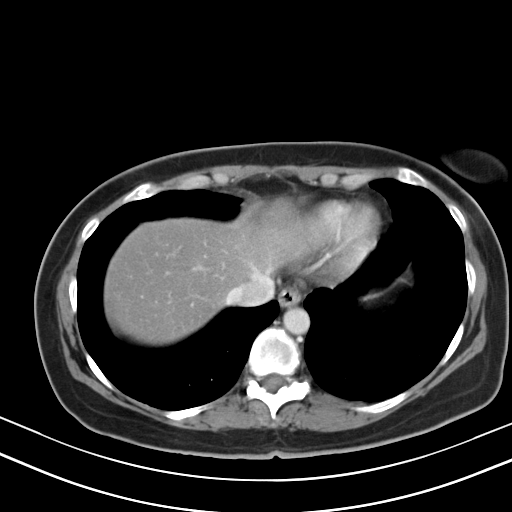
Contrast-enhanced abdominal CT, one axial slice; position 42 of 47 along the scan axis; reconstruction kernel B40s; soft-tissue window (W 400 / L 40 HU); 5 mm slice thickness; 512 × 512 image matrix, field of view 350 × 350 mm. Female patient. Case-level facts recorded for this patient, not image findings: diagnosis: colorectal cancer liver metastases, imaged before liver resection; multiple liver metastases: no; largest metastasis: 3.5 cm; disease in both lobes: no.
Outlined on this slice (expert manual segmentation):
- hepatic veins: box from (x=226, y=257) to (x=271, y=304) px
- liver: (x=107, y=221)–(x=301, y=340)
- planned liver remnant (the part of the liver to remain after resection): (x=107, y=221)–(x=301, y=341)